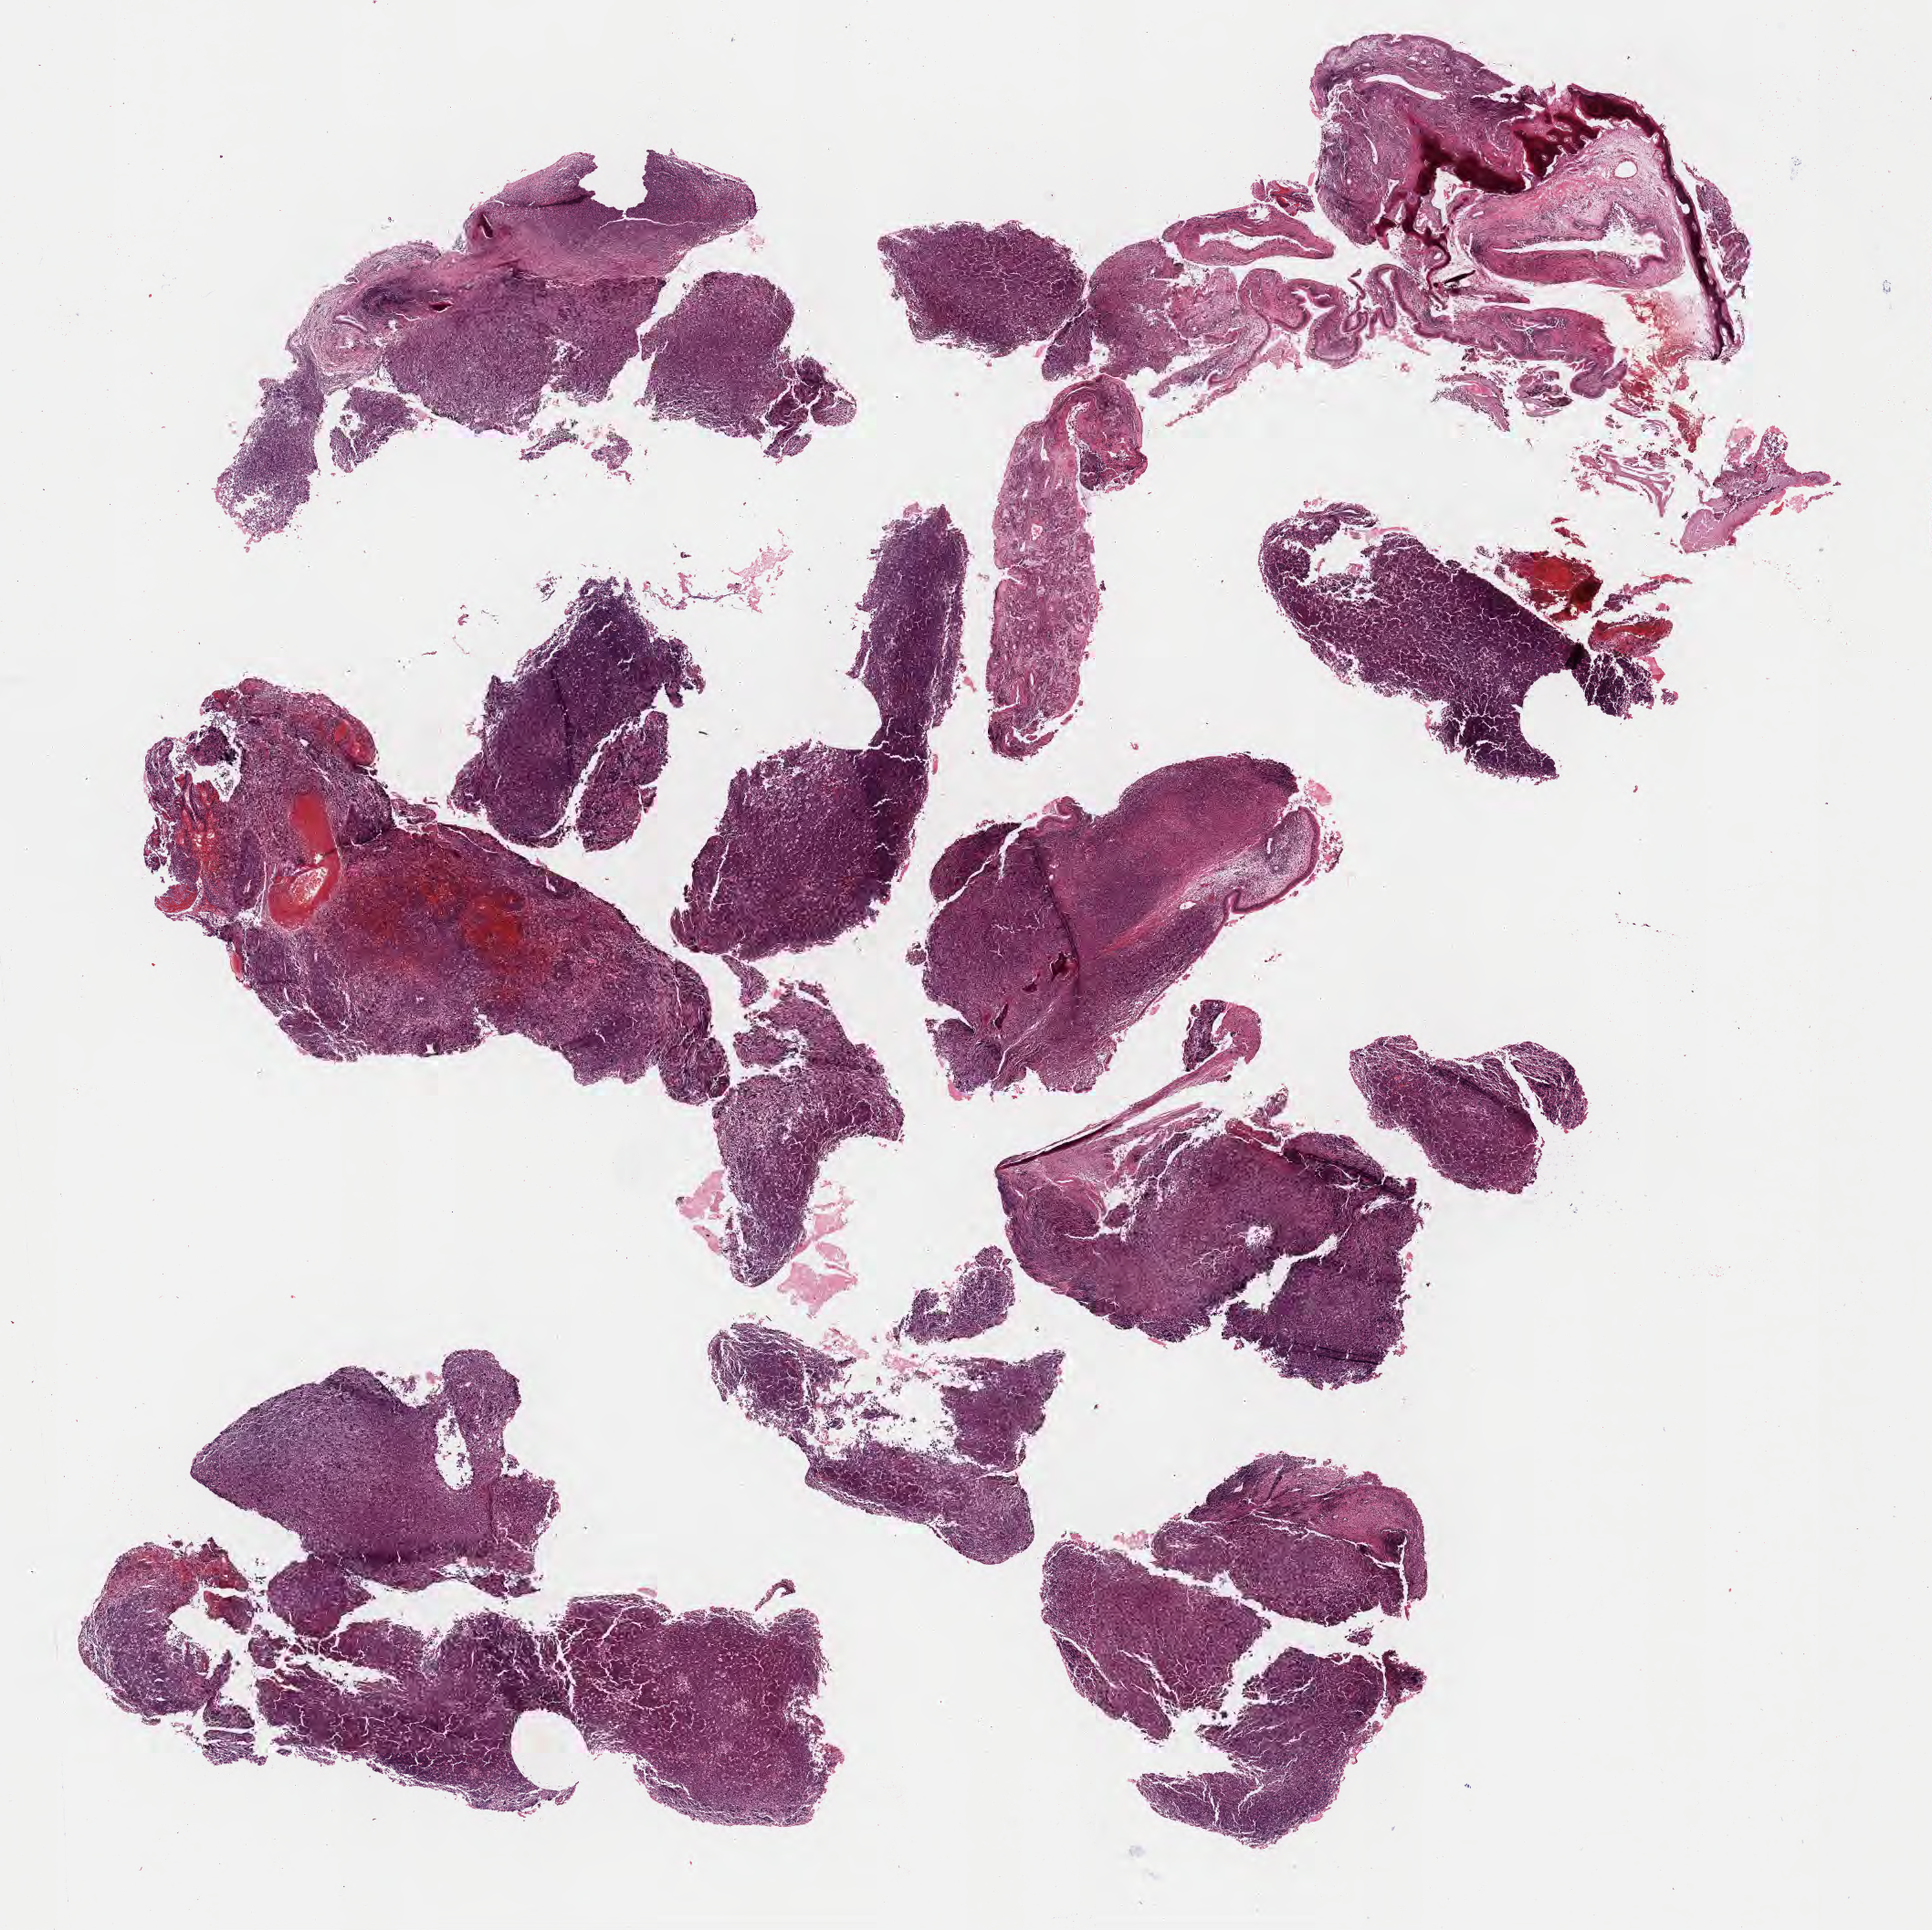
Digitized H&E-stained section — shown as a low-resolution overview of the whole scanned area (about 17.1 x 17.1 mm); formalin-fixed paraffin-embedded section; specimen: primary tumor. Patient male; aged 38. Composition of this section per pathologist review: tumor cells 80%, tumor nuclei 85%, stromal cells 10%, necrosis 10%, normal cells 0%. Inflammatory infiltration, as recorded: lymphocyte infiltration 50%, monocyte infiltration 25%, neutrophil infiltration 5%.
• diagnosis: Burkitt lymphoma, NOS
• Ann Arbor stage (patient): Stage I